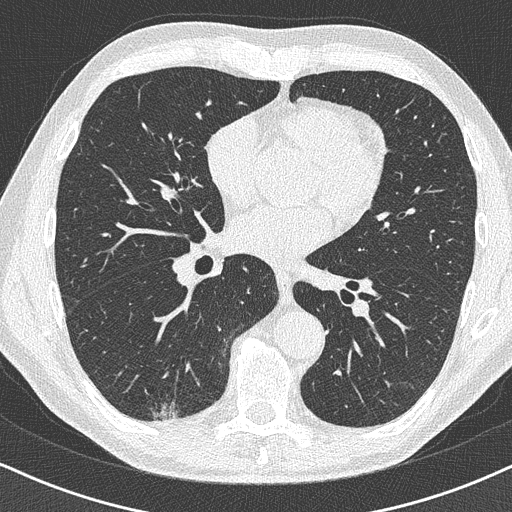
Low-dose screening chest CT, axial slice; baseline annual screen; lung window (W 1500 / L -600 HU); 1 mm slice thickness; lung (sharp) reconstruction kernel (B50f); slice 229 of 438 in the series. Male participant, aged 63 years at enrolment.
- Expert-annotated lung lesion, bounding box [x1, y1, x2, y2] px = [126, 355, 198, 427].
- The exam's reader record, not a measurement of the box and not confirmed to be the same lesion: non-calcified nodule or mass ≥4 mm, right lower lobe, 16 × 13 mm, poorly defined margins.
- Official screen result: positive, change unspecified: nodule(s) >= 4 mm or enlarging nodule(s), mass(es), or other non-specific abnormalities suspicious for lung cancer.
- Later outcome: lung cancer diagnosed 74 days after this screen — adenocarcinoma, NOS, right lower lobe, moderately differentiated (G2), stage IA (AJCC 6th edition), 20 mm at pathology.